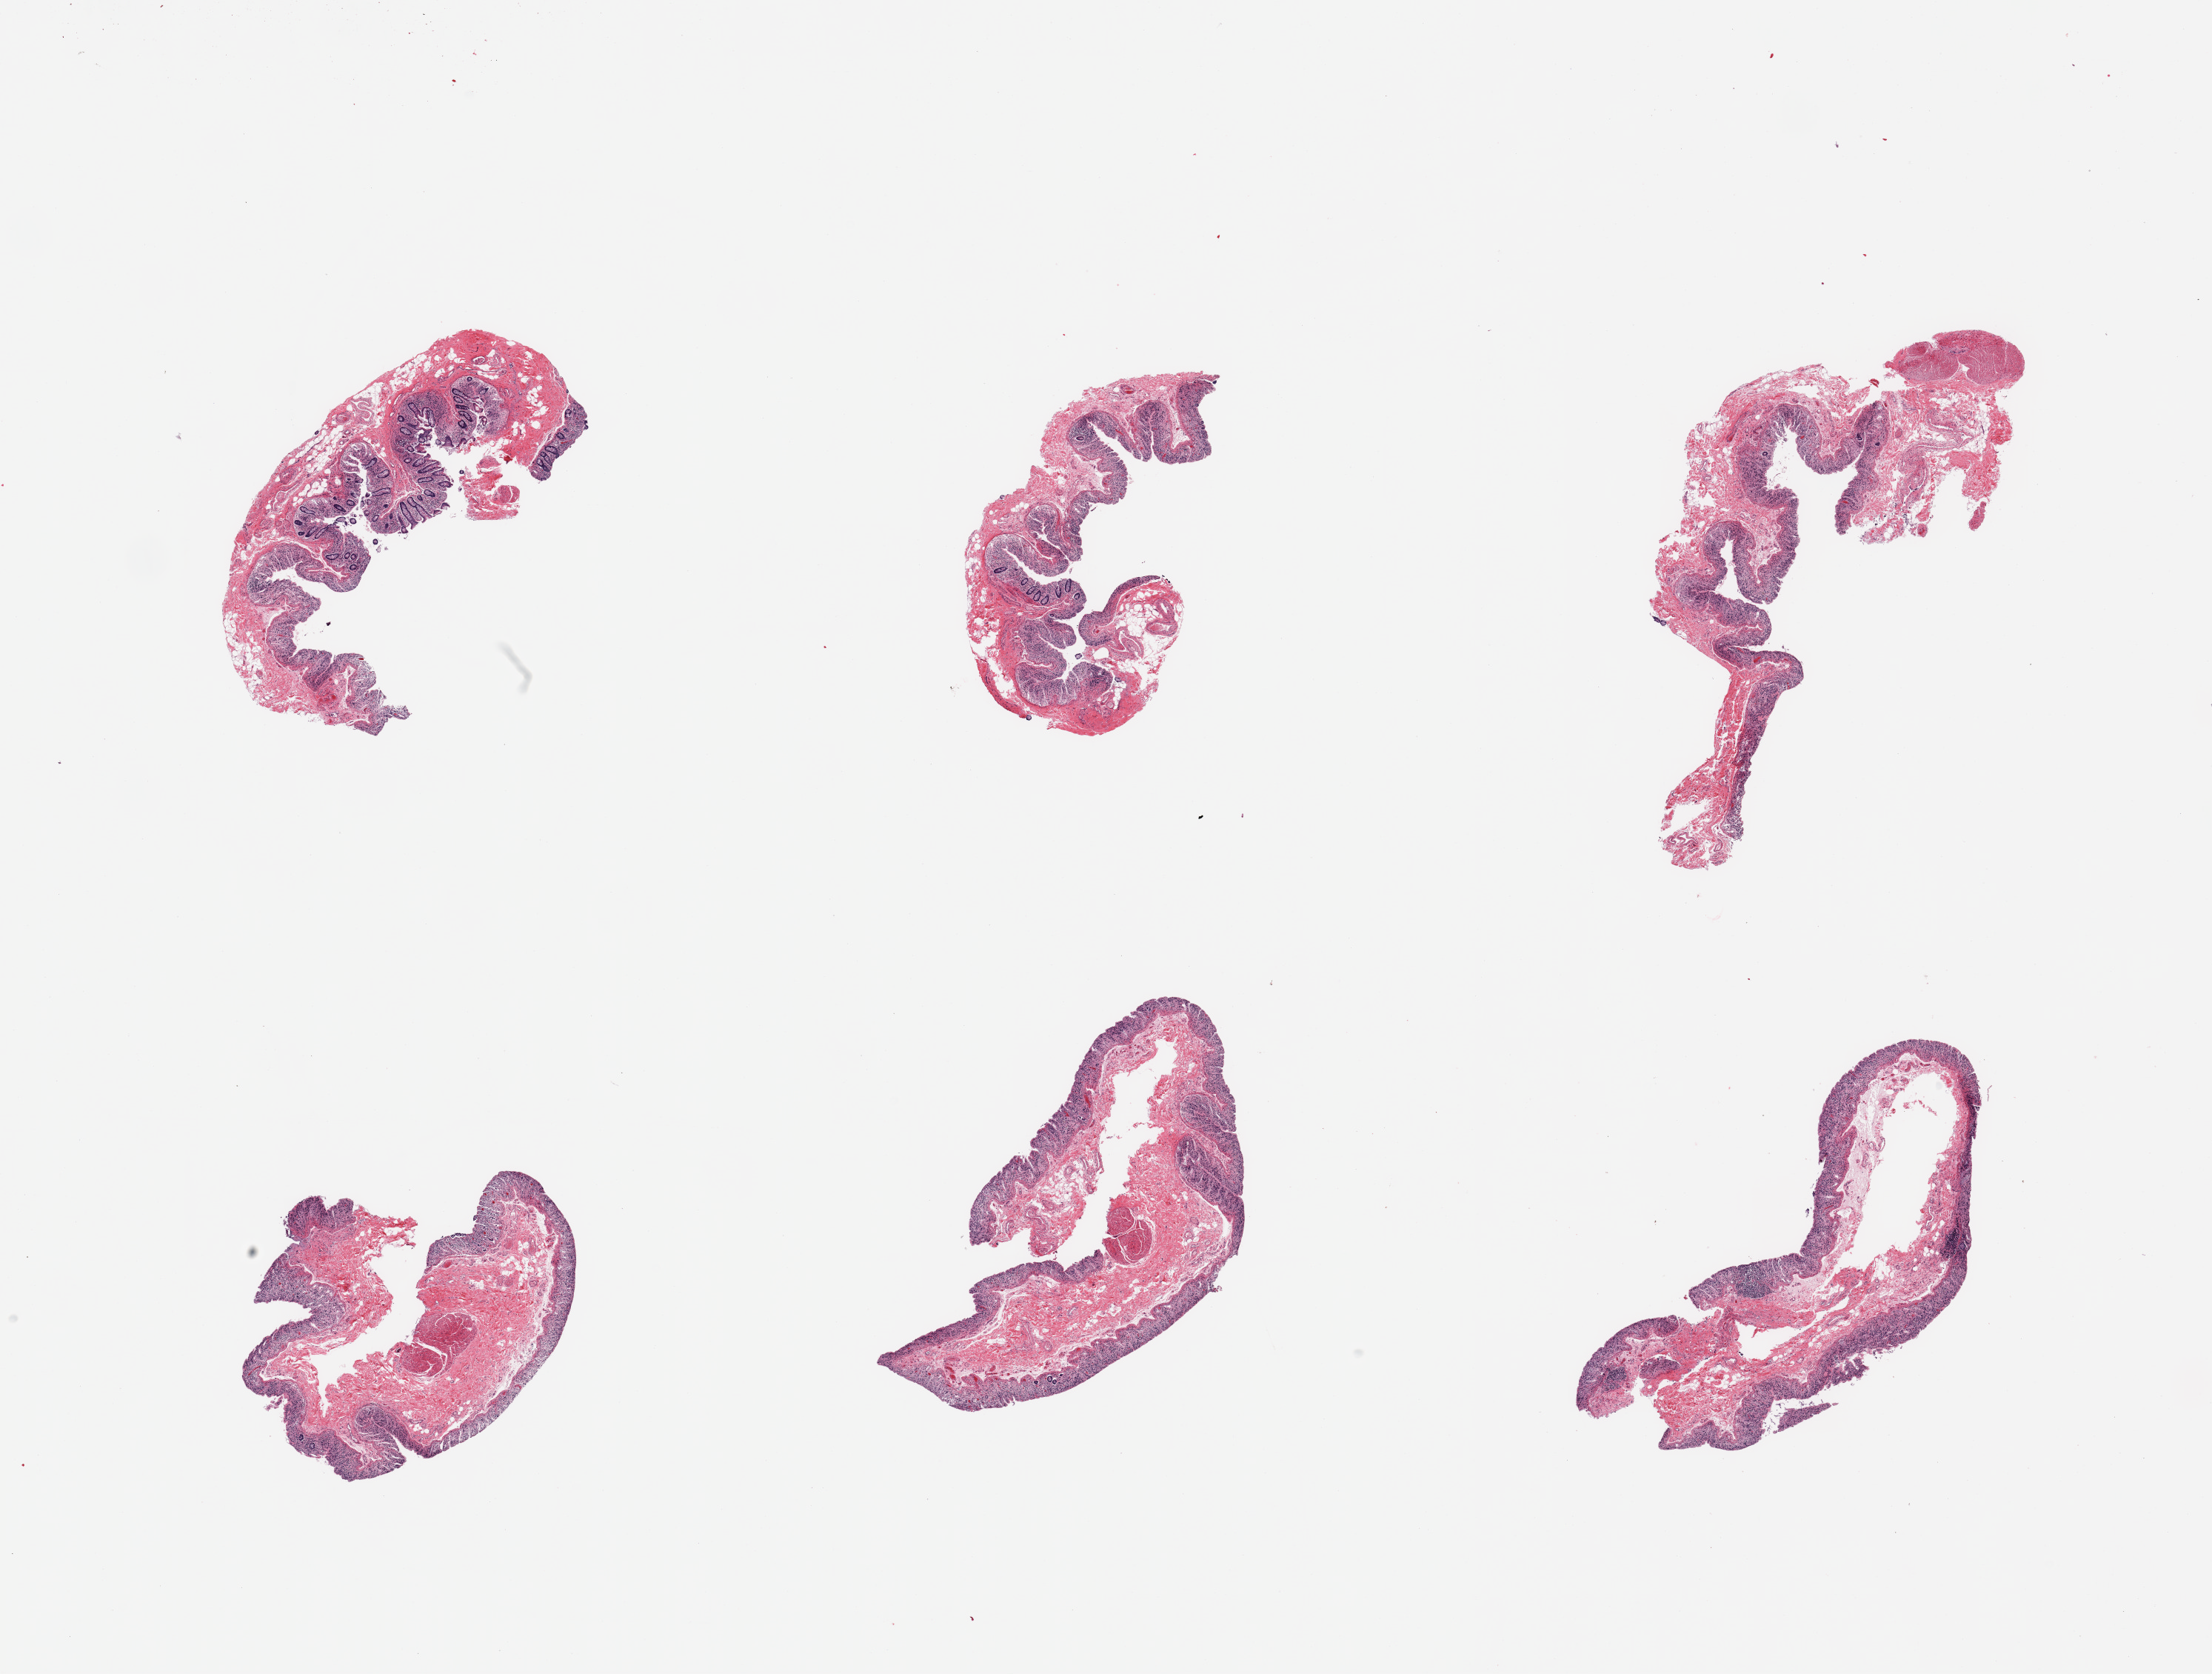
Hematoxylin and eosin (H&E) whole-slide image, a low-resolution overview of the entire scanned area, about 23.6 x 17.9 mm, PAXgene-fixed, paraffin-embedded tissue, sampled site (target tissue): transverse colon, tissue donor sample. Male donor.
* pathologist's review note for this sample: 6 pieces; moderate to severe mucosal autolysis; few pieces contain small fragments of muscularis